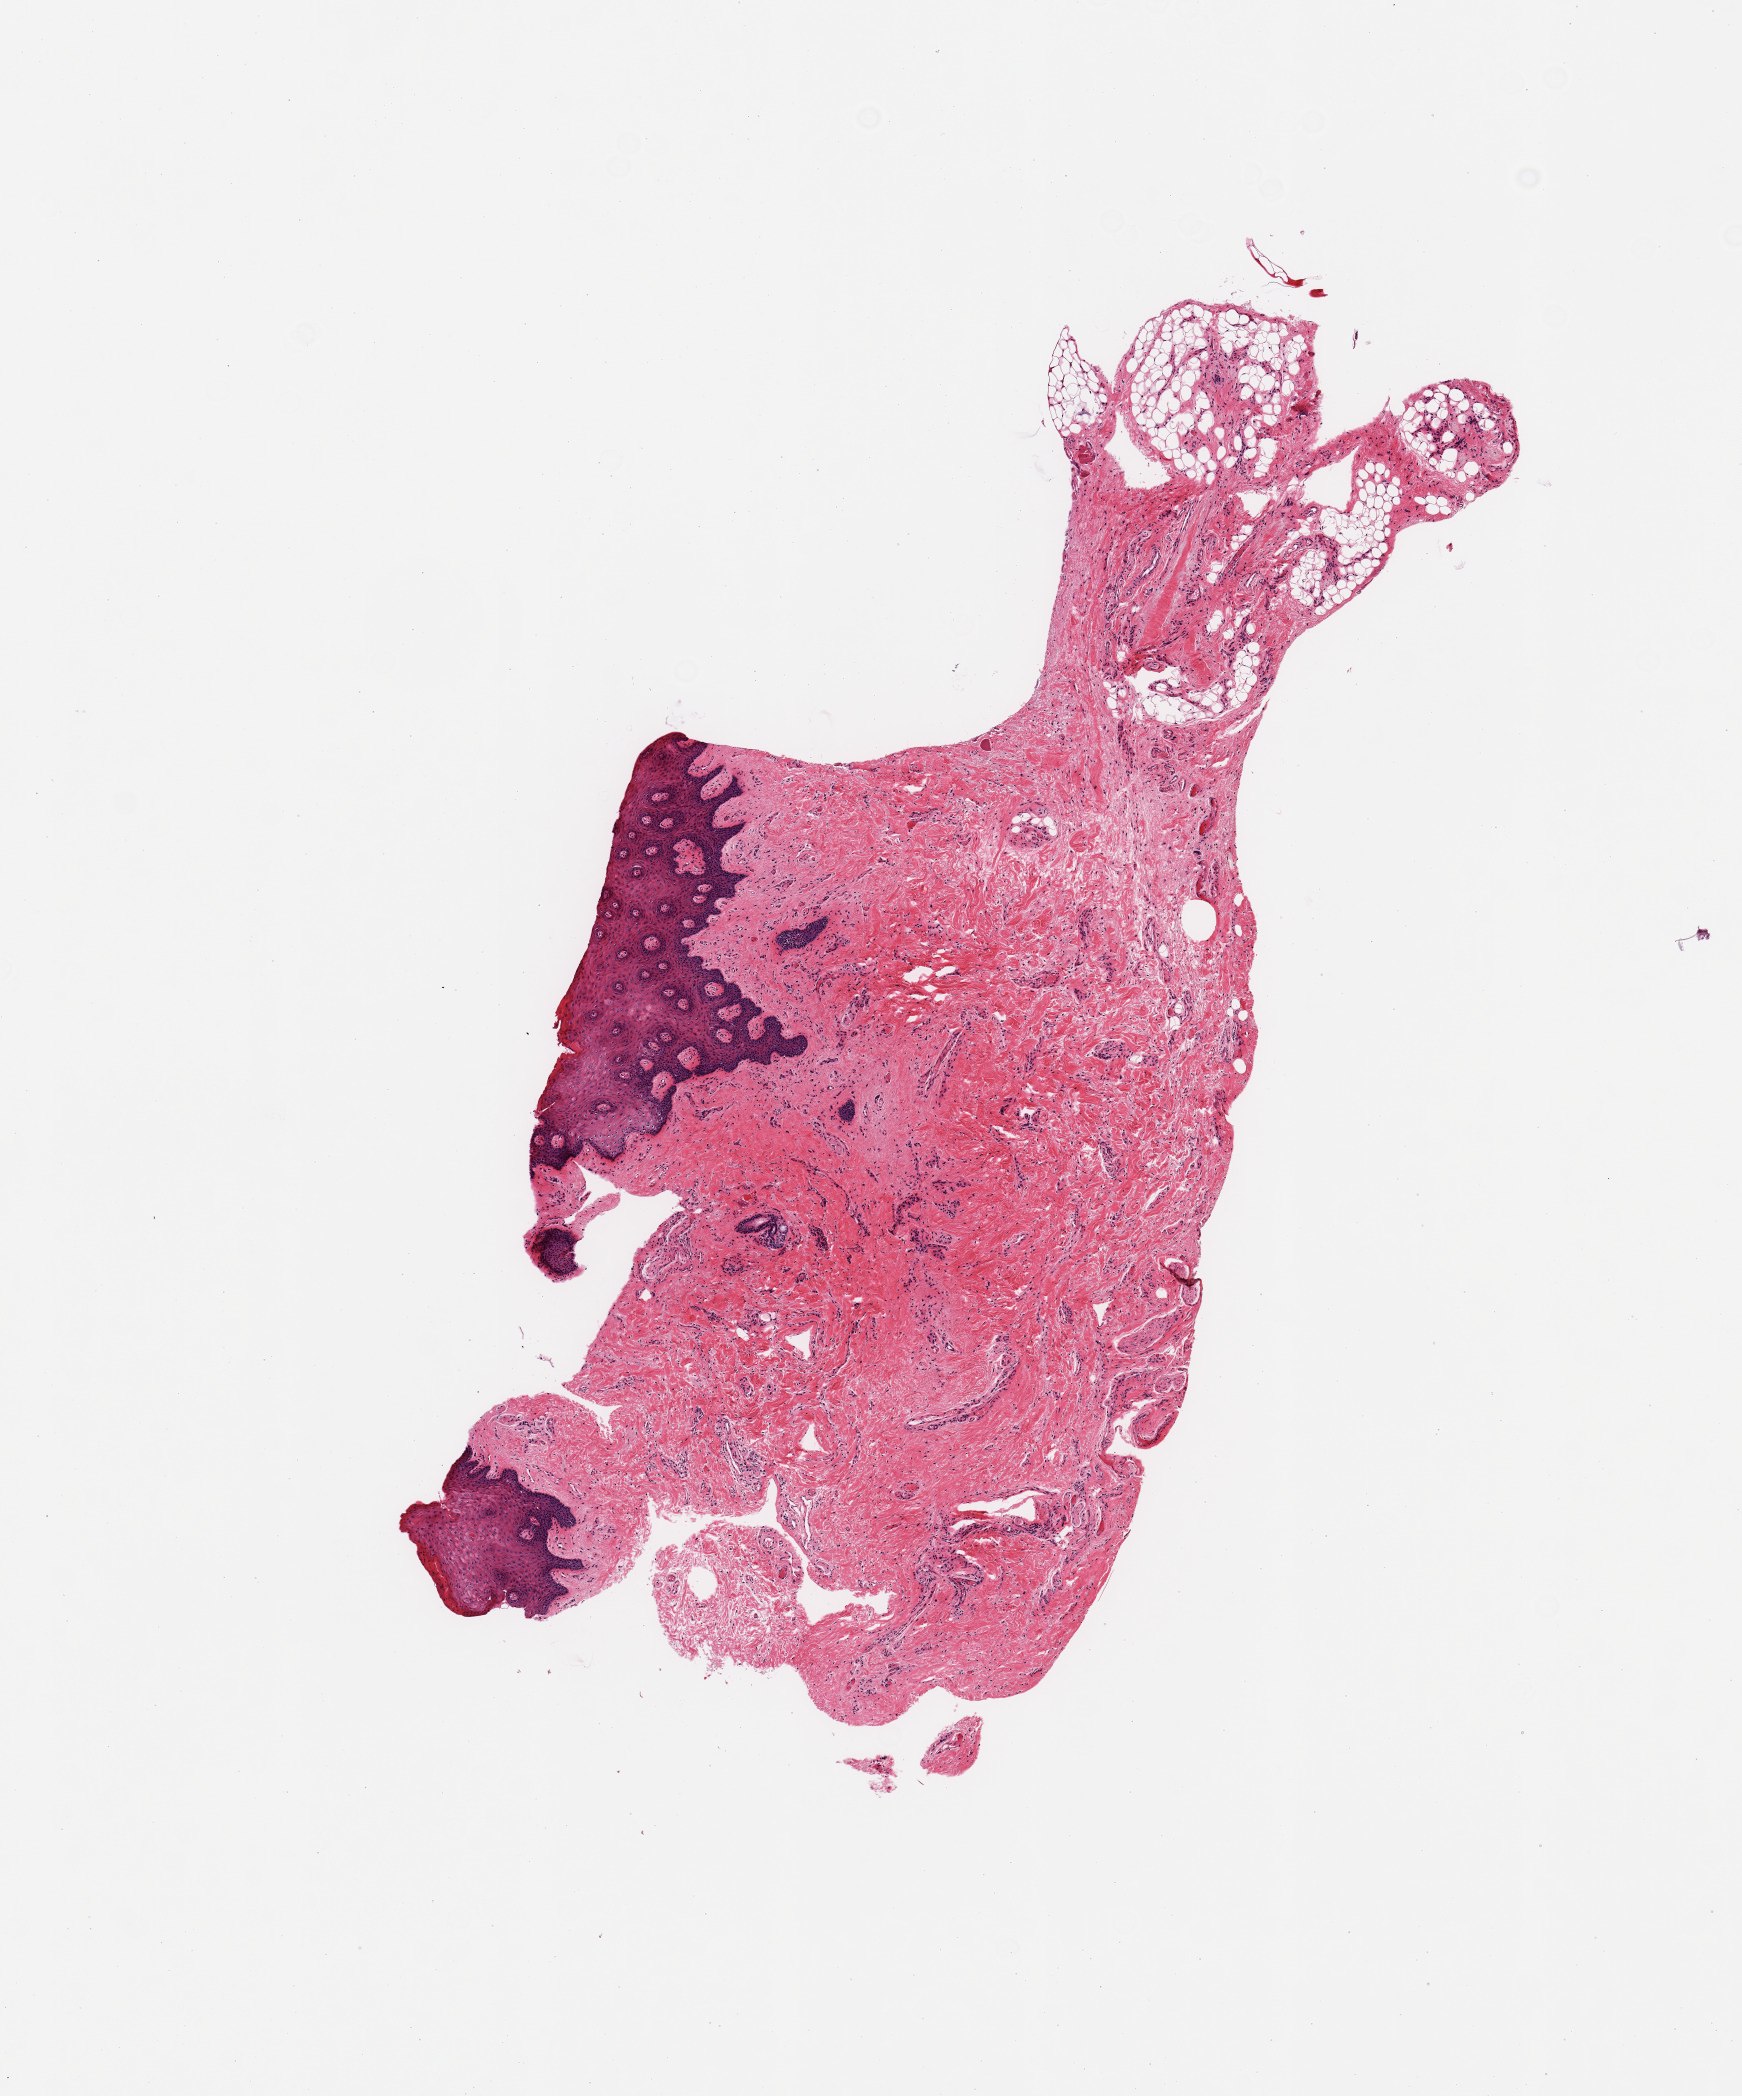
Hematoxylin and eosin (H&E) whole-slide image, whole scanned area (about 6.9 x 8.3 mm) shown as a low-resolution overview, PAXgene-fixed, paraffin-embedded tissue, target tissue: minor salivary gland, tissue donor sample. Male donor.
Pathologist's review note for this sample: 1 piece; lip, stroma, and fat.